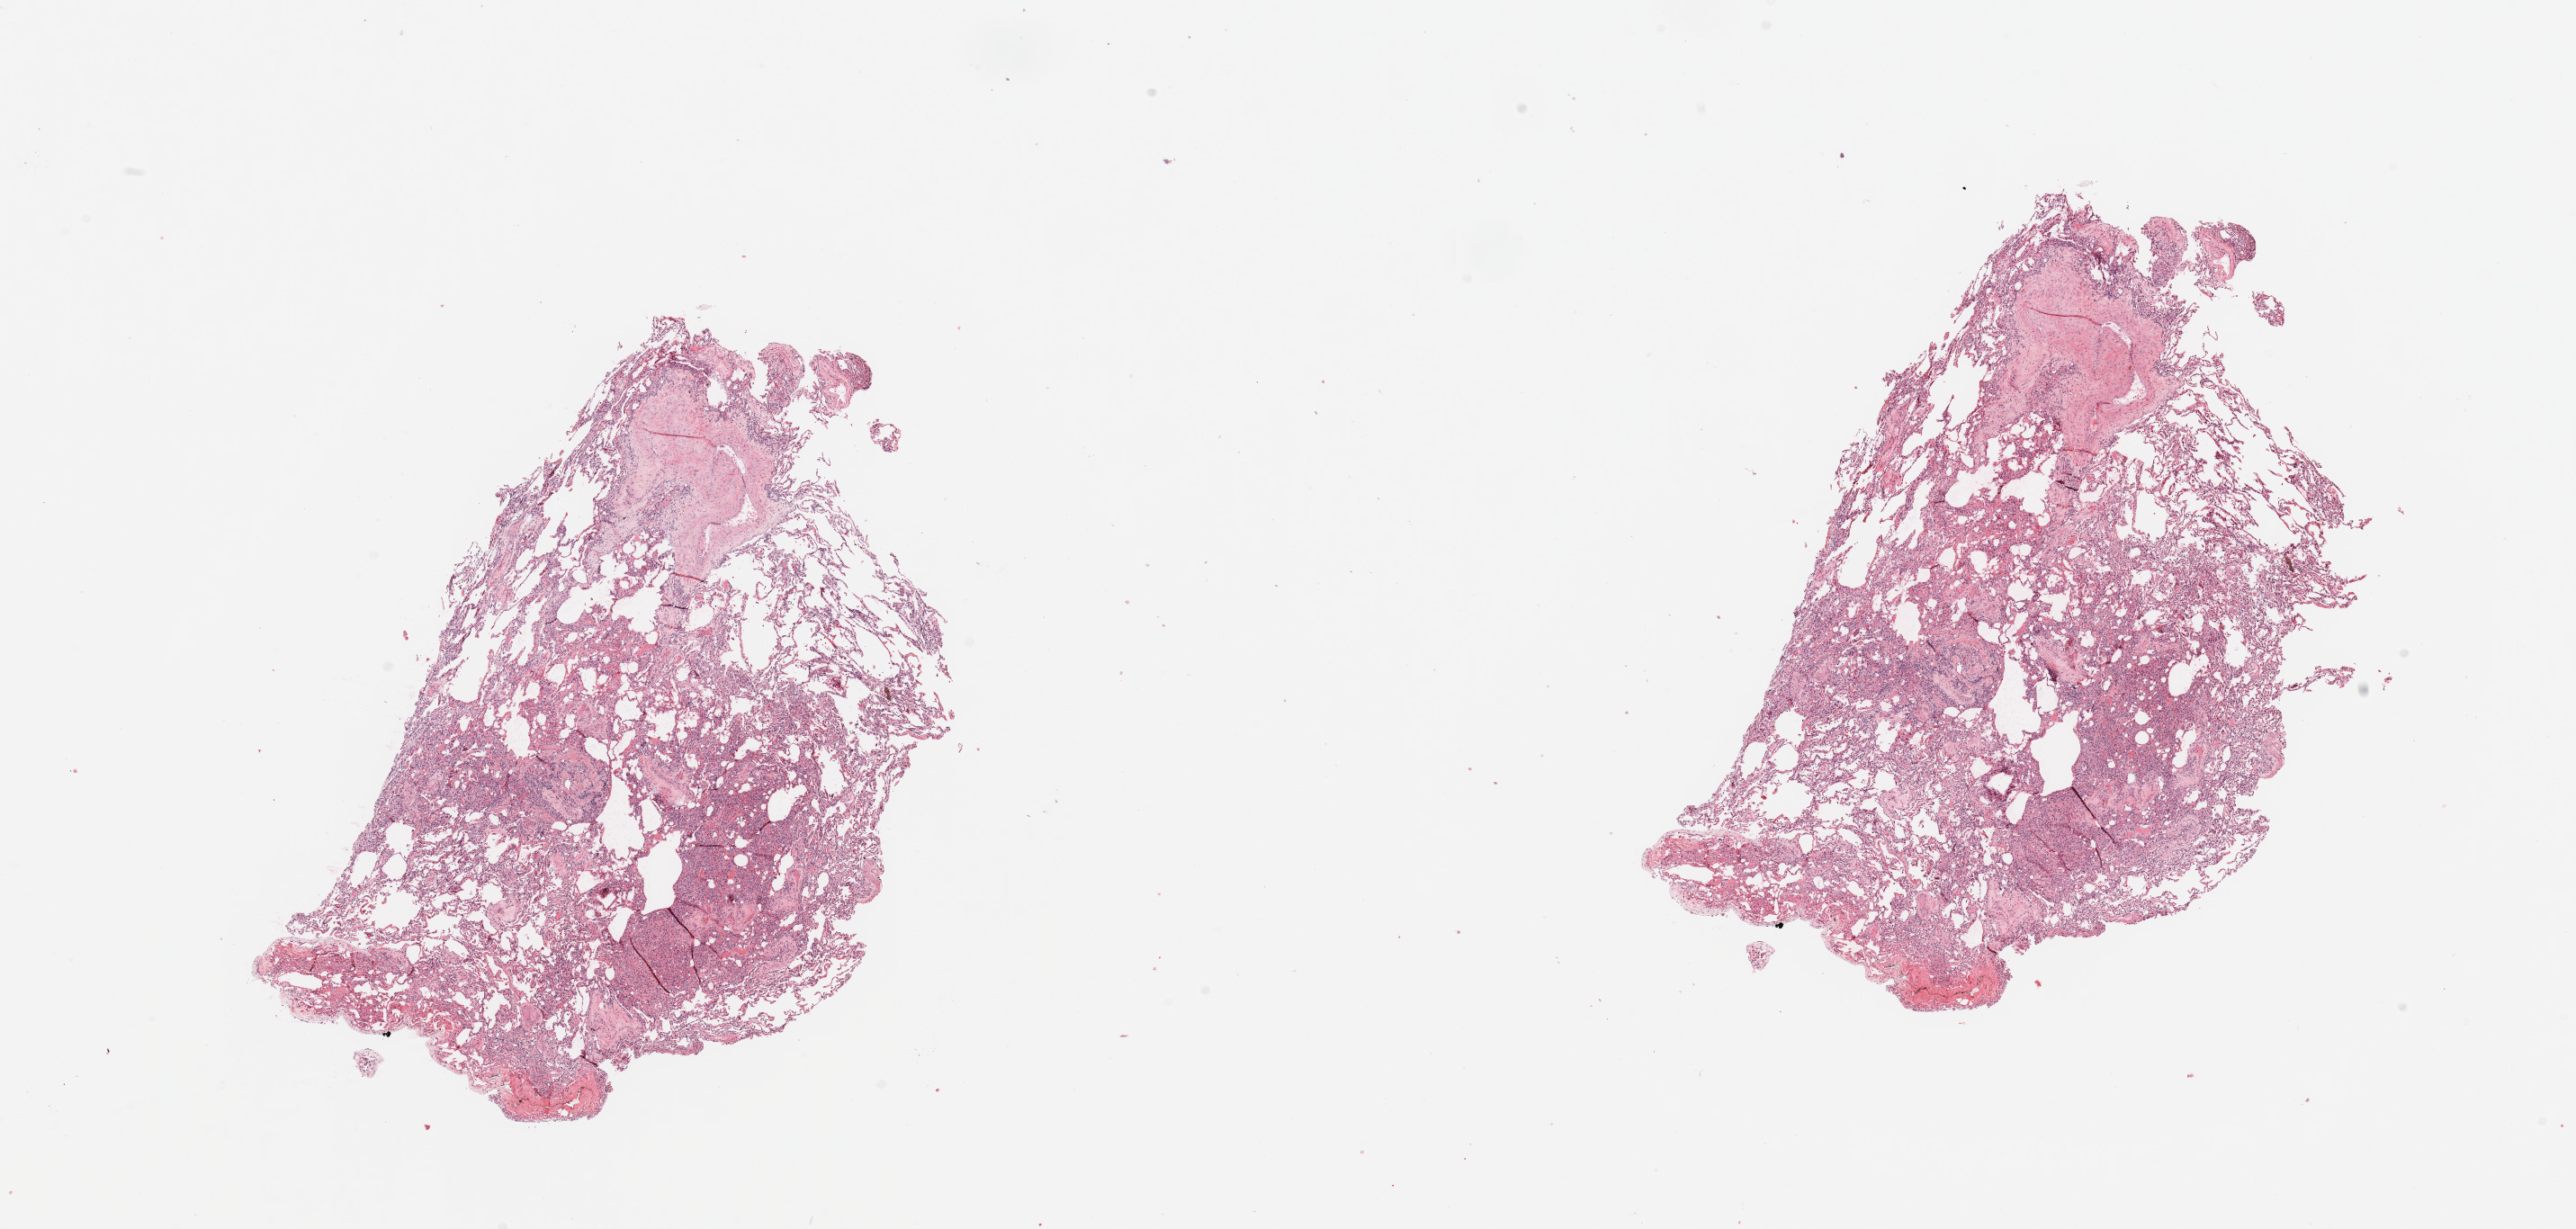
Whole-slide histology image, Hematoxylin and eosin (H&E) stained — a low-resolution overview of the entire scanned area, about 22.6 x 10.8 mm. Normal (non-tumour) tissue sample, sampled site: lung. Patient: male, age 61 years.
This section: normal (non-tumour) tissue from the same patient. Patient diagnosis: Squamous cell carcinoma, NOS.